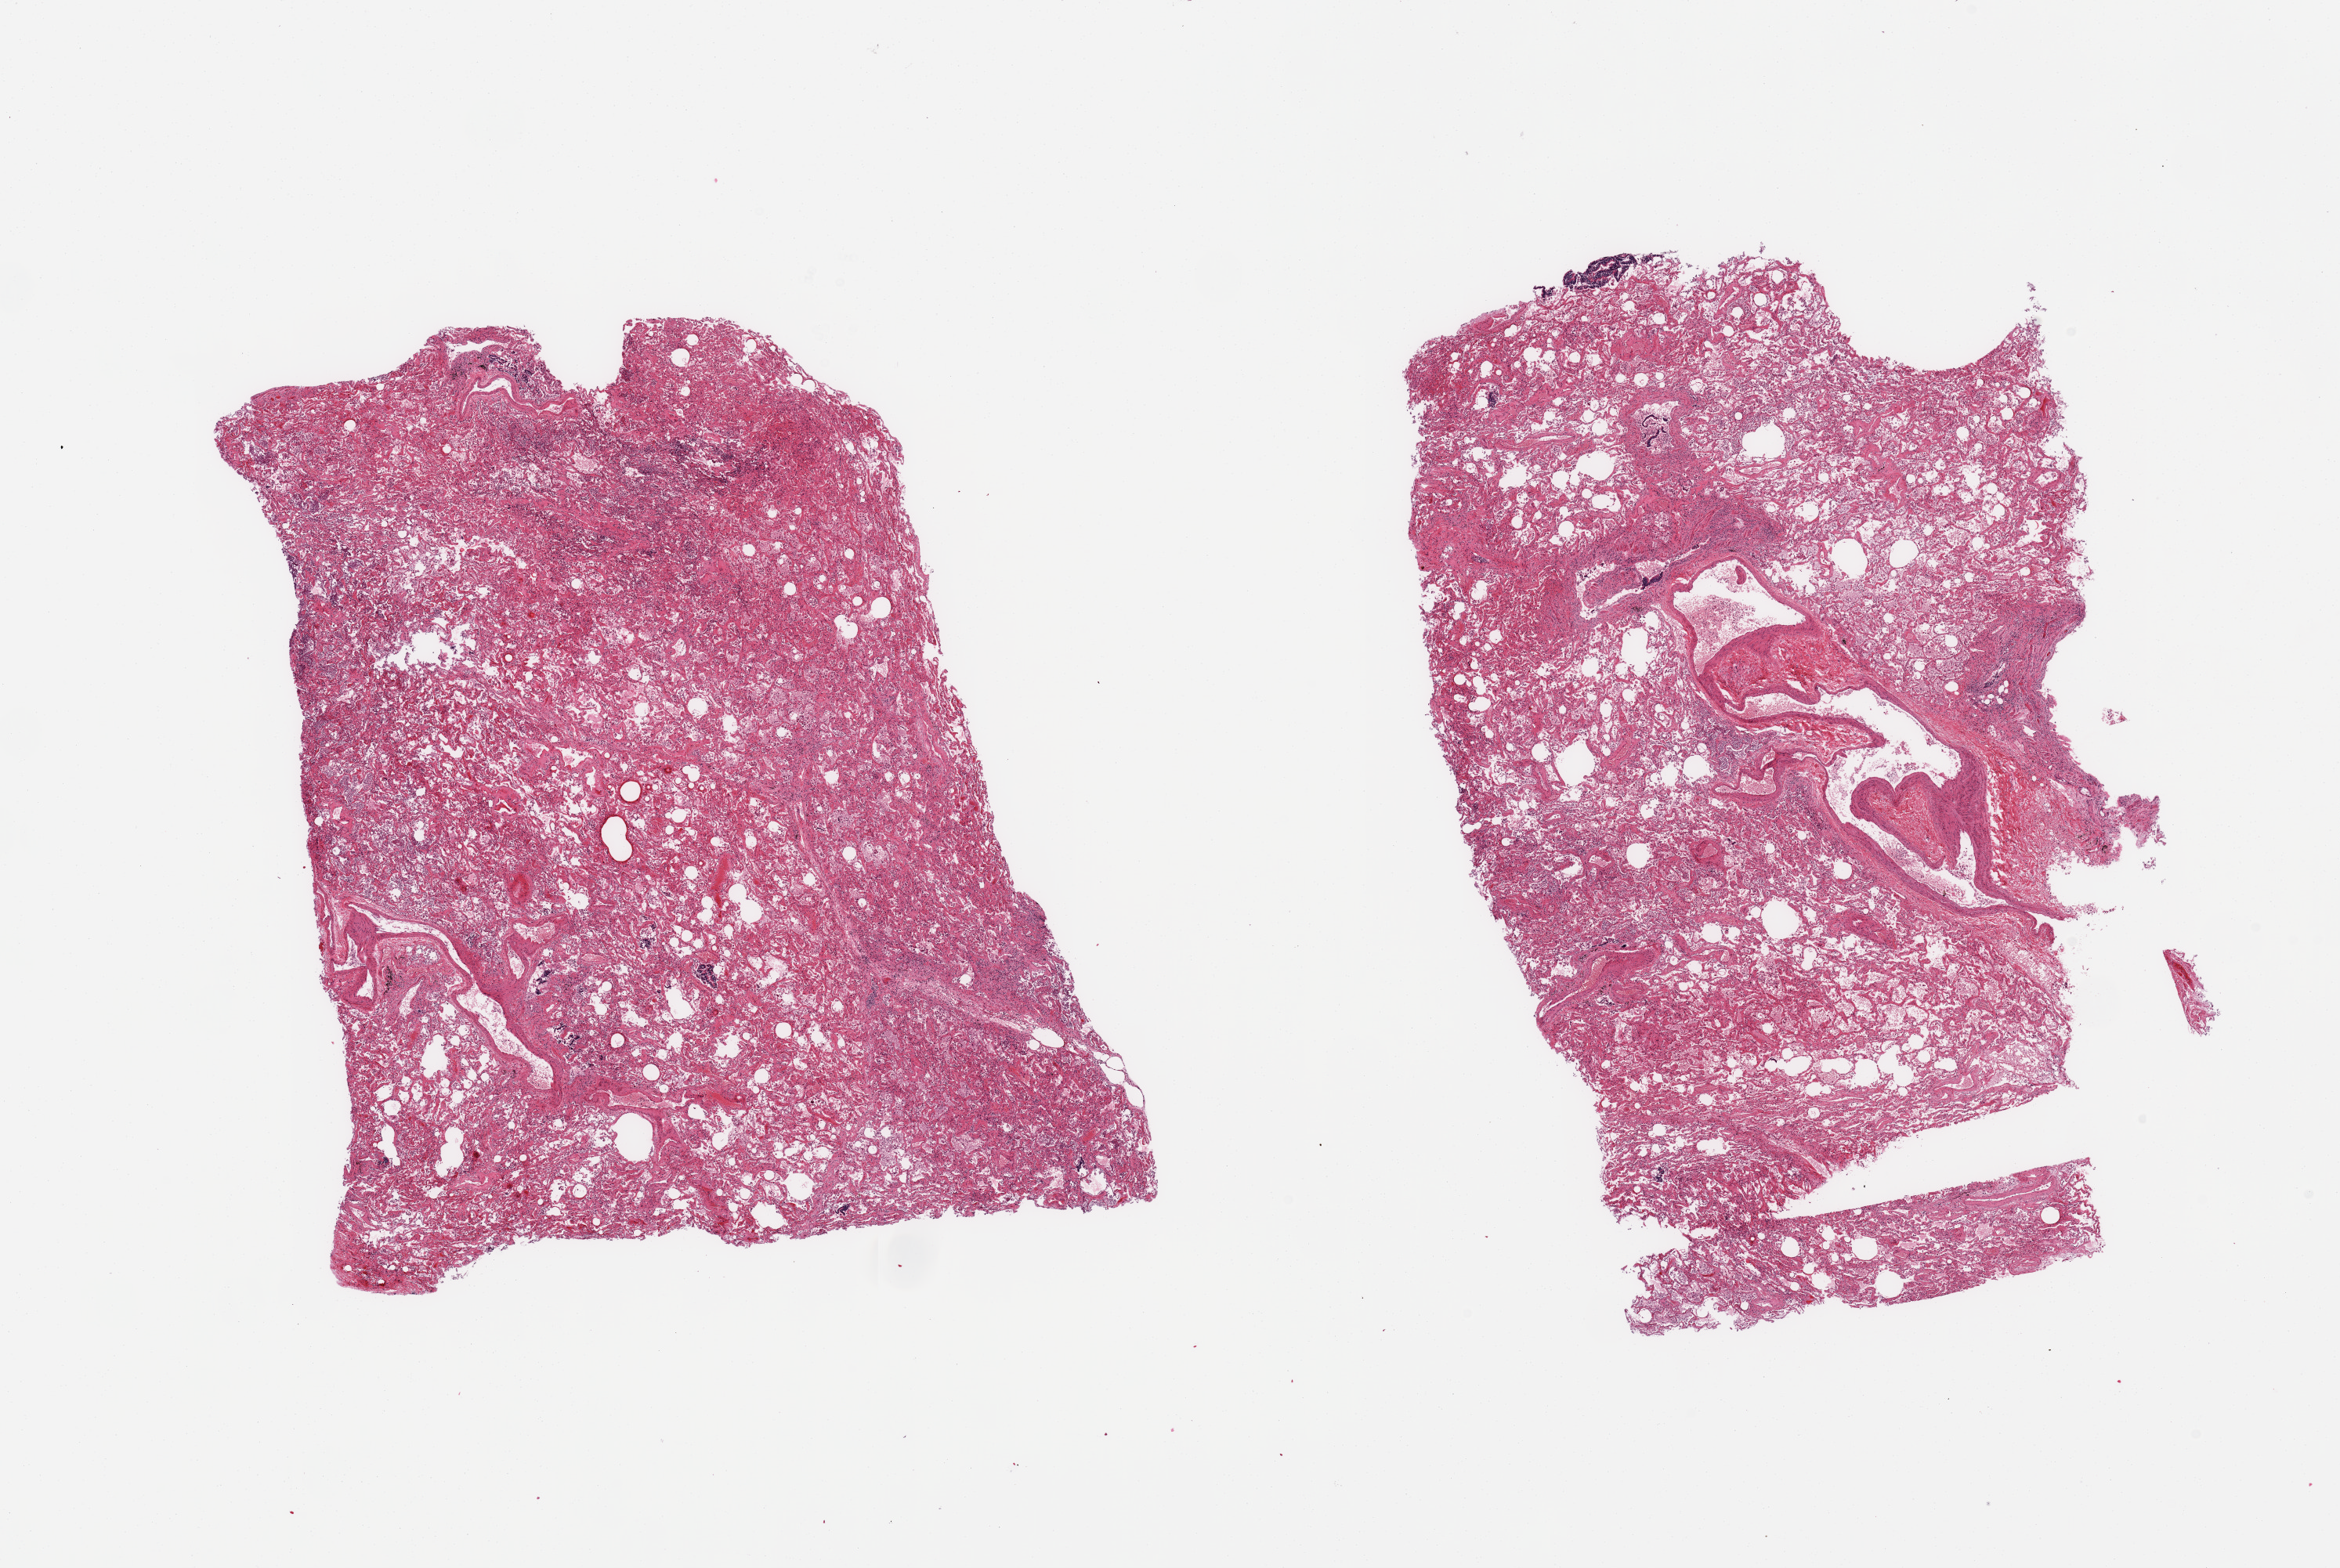
Digitized hematoxylin and eosin (H&E)-stained section, brightfield — a low-resolution overview of the entire scanned area, about 23.6 x 15.8 mm. PAXgene-fixed, paraffin-embedded tissue. Target tissue: lung. Donor tissue sample. Donor sex: female.
Pathologist's review note for this sample: 2 pieces; moderate diffuse alveolar fibrosis; edema and patchy pneumonia.